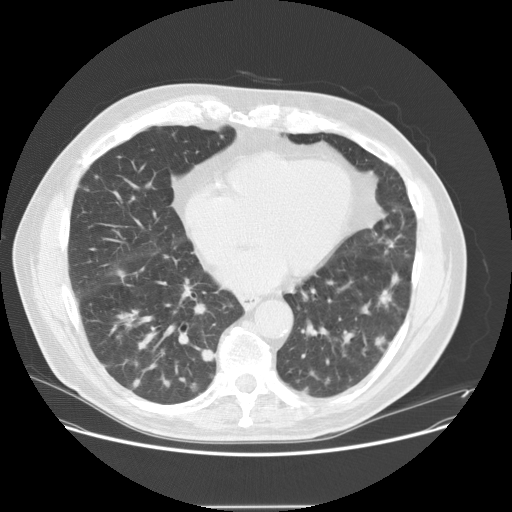
Low-dose screening chest CT, one axial slice; slice 58 of 143 in the series (ordered by position); lung window (W 1500 / L -600 HU); 2.5 mm slice thickness; 512 × 512 image matrix, field of view 400 × 400 mm.
Annotated regions visible in this slice (manually delineated by an expert):
- lesion 1 (tumor, lower lobe of right lung): box from (x=201, y=349) to (x=214, y=362) px